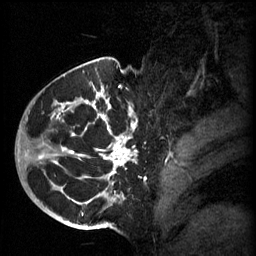
Breast MRI (dynamic contrast-enhanced), one sagittal slice. Position 42 of 60 along the scan axis. 3 images stored at this slice position (order not interpretable as contrast timing). 1.5 T. TE 4.2 ms, TR 11 ms. 2 mm slice thickness. 256 × 256 image matrix, field of view 200 × 200 mm. Patient: female, 51 years.
Annotated regions visible in this slice (semi-automatically segmented with operator editing):
- analysis volume of interest (the breast-tissue region the enhancement analysis was run in; not a lesion): bounding box <48,82,161,197> (left, top, right, bottom; pixels)
- tumour enhancement mask (voxels above the 70 % enhancement threshold inside the analysis volume of interest): <48,86,137,197>